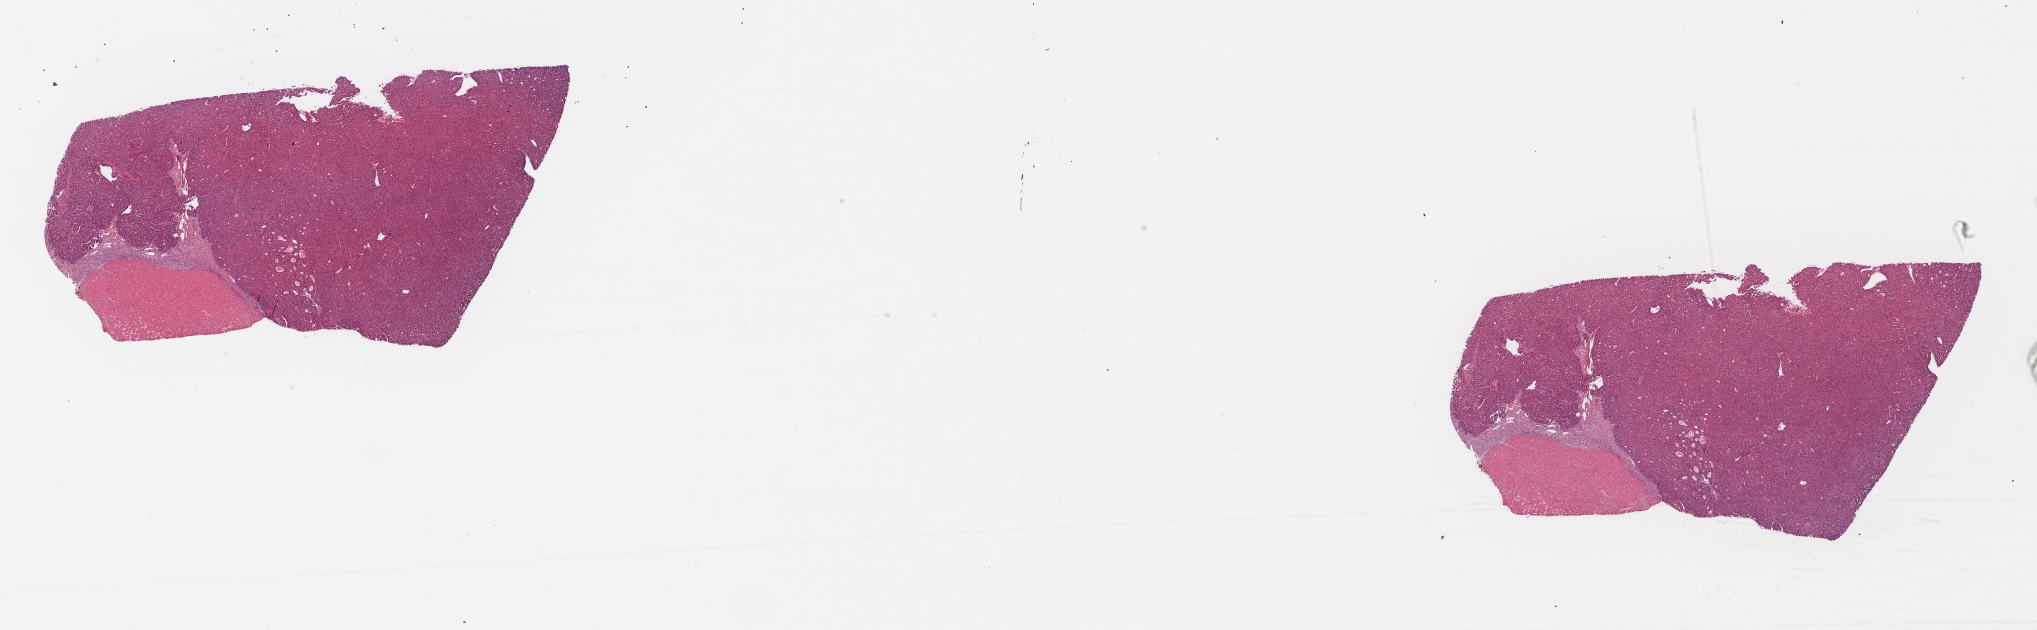
Whole-slide histology image, Hematoxylin and eosin (H&E) stained — shown as a low-resolution overview of the whole scanned area (about 32.0 x 9.9 mm, from a 40x scan), formalin-fixed paraffin-embedded (FFPE) diagnostic section, primary tumour sample from the liver. Patient: male, age at initial diagnosis 62 years. Histologic grade: G1 (well differentiated).
AJCC pathologic stage: I (7th edition). Diagnosis: Hepatocellular carcinoma, NOS.